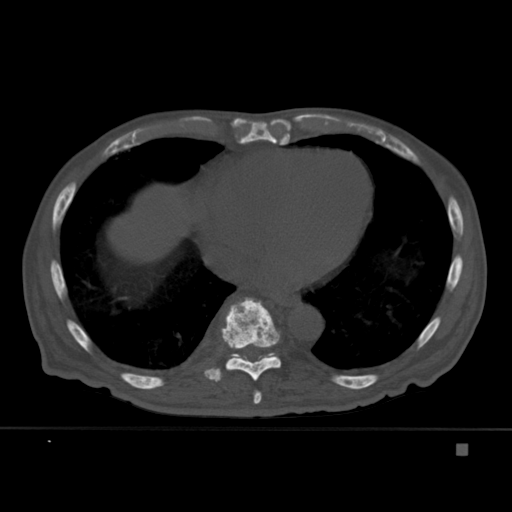
CT including the spine, one axial slice; position 246 of 451 along the scan axis; bone window (W 1800 / L 400 HU); 1.5 mm slice thickness; 512 × 512 image matrix. Patient: male, 75 years. Case-level facts recorded for this patient, not image findings: primary cancer: prostate.
Annotated regions visible in this slice (semi-automatically segmented with operator editing):
- T10 vertebra: bounding box (x1, y1, x2, y2) in pixels: (230, 353, 275, 358)
- T8 vertebra: (253, 390, 262, 404)
- T9 vertebra: (204, 297, 281, 382)